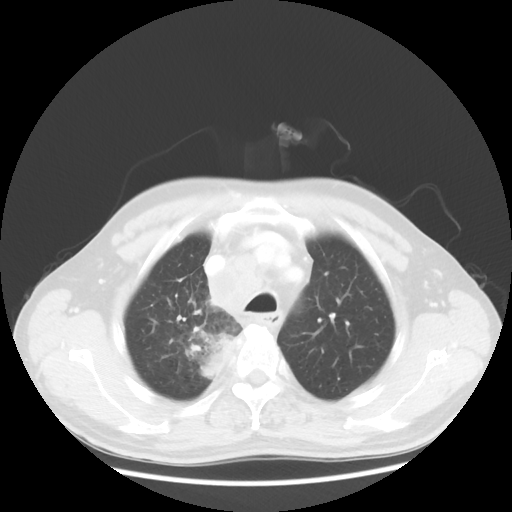
Chest CT, one axial slice. Slice 97 of 124 in the series (ordered by position). Reconstruction kernel STANDARD. Lung window (W 1500 / L -600 HU). 5 mm slice thickness. 512 × 512 image matrix, field of view 382 × 382 mm. Male patient, age 64 years. Case-level facts recorded for this patient, not image findings: clinical TNM (as recorded): T3 N3 M0.
Structures marked on this image (rectangle marked by the reading radiologist):
- lung tumour (recorded histology: small cell carcinoma): box from (x=187, y=323) to (x=242, y=386) px